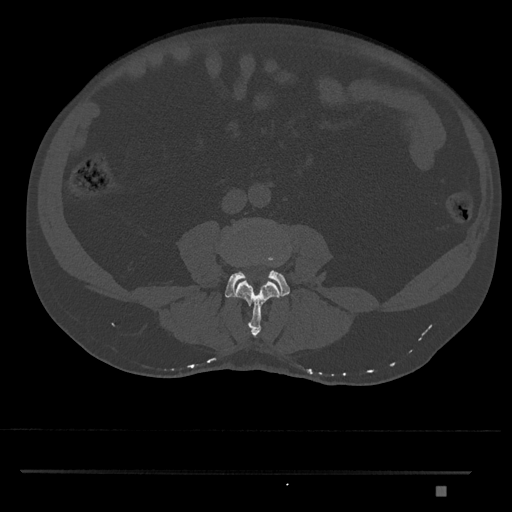
CT including the spine, one axial slice; position 651 of 1134 along the scan axis; bone window (W 1800 / L 400 HU); 512 × 512 image matrix. Male patient, age 65 years. Case-level facts recorded for this patient, not image findings: primary cancer: prostate.
Outlined on this slice (semi-automatically segmented with operator editing):
- L3 vertebra: bounding box <235,281,280,338> (left, top, right, bottom; pixels)
- L4 vertebra: <225,256,290,298>